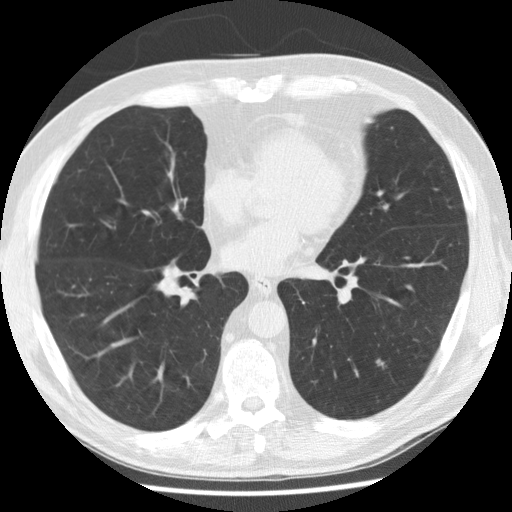
Chest CT (low-dose screening protocol), one axial image, first (baseline) screen, lung window (W 1500 / L -600 HU), 2.5 mm slice thickness, slice 149 of 265 in the series, 512 × 512 image matrix. Male, age 58 years at enrolment. Former smoker at enrolment.
Lesion marked by an expert reader, bounding box (x1, y1, x2, y2) in pixels: (367, 348, 399, 379). Screening reader's record for this exam: no non-calcified nodule ≥4 mm recorded. Official screen result: negative screen, no significant abnormalities.